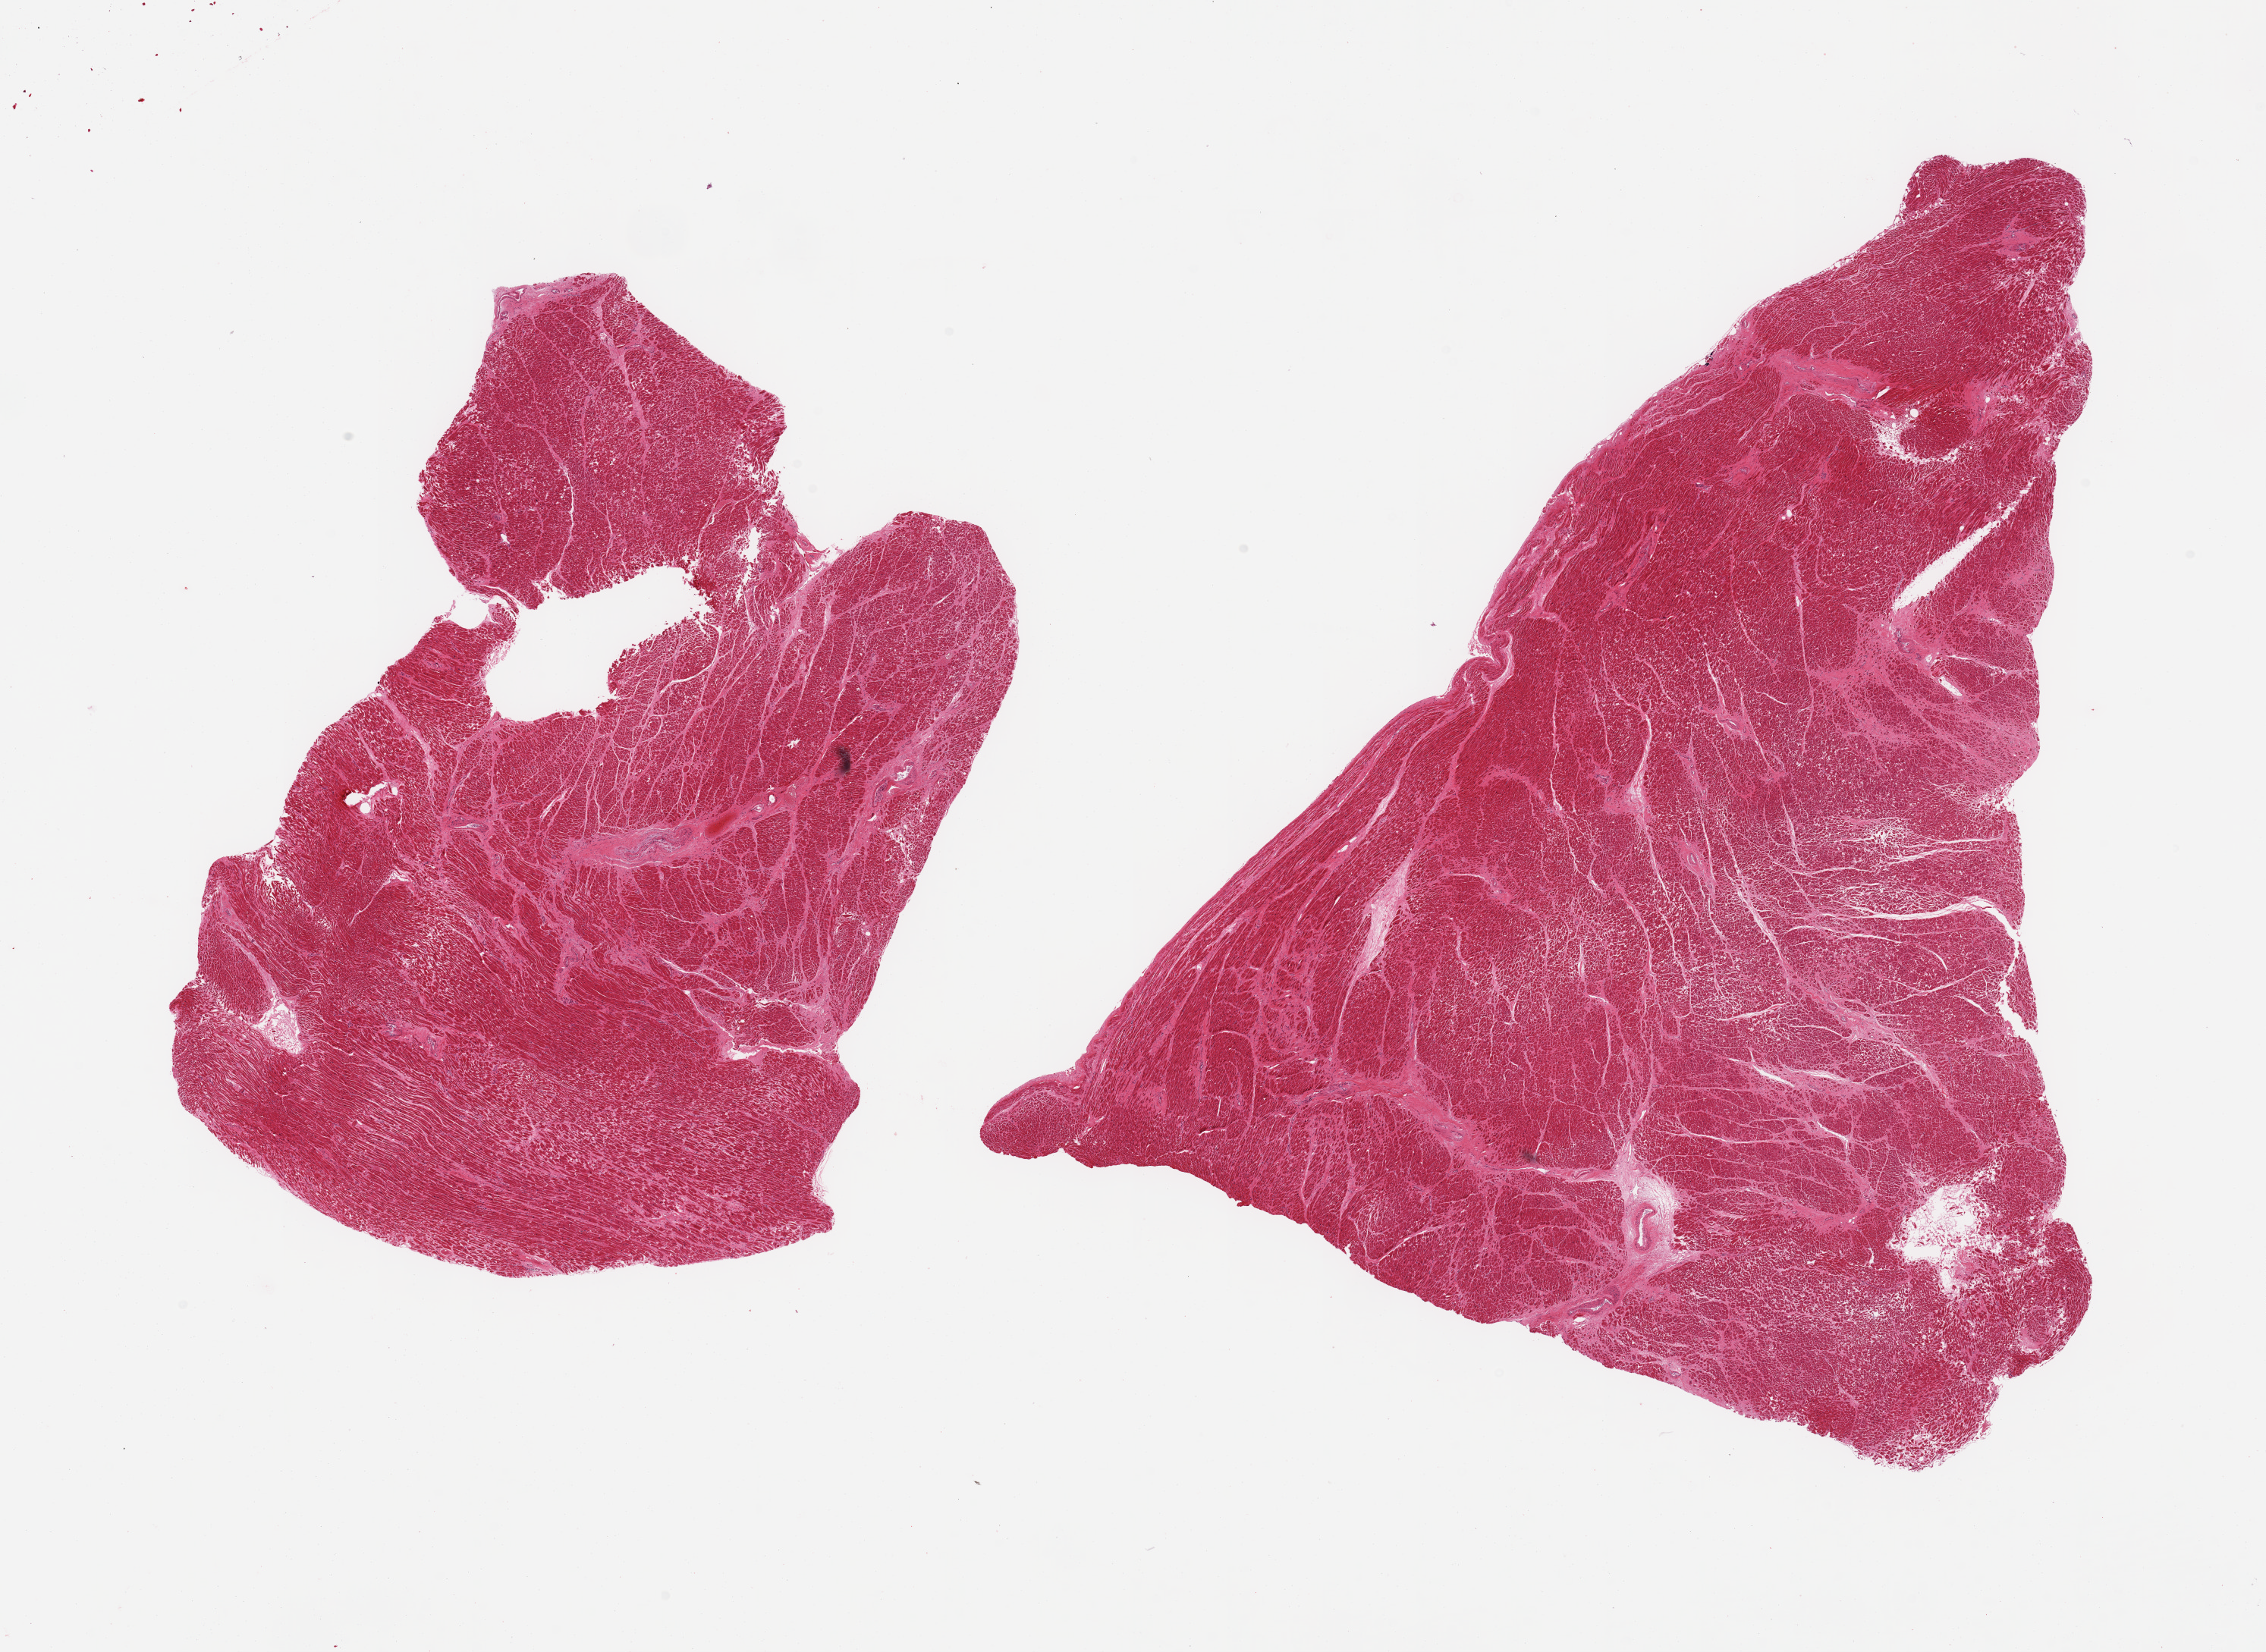
Digitized haematoxylin and eosin-stained section, brightfield — low-resolution overview of the scanned area, about 23.6 x 17.2 mm (acquisition: 20x scan), PAXgene-fixed, paraffin-embedded tissue, section of heart (target tissue), donor tissue sample. Male donor.
- pathologist's review note for this sample: 2 pieces, marked chronic ischemic damage, remote infarcts up to ~2.5mm